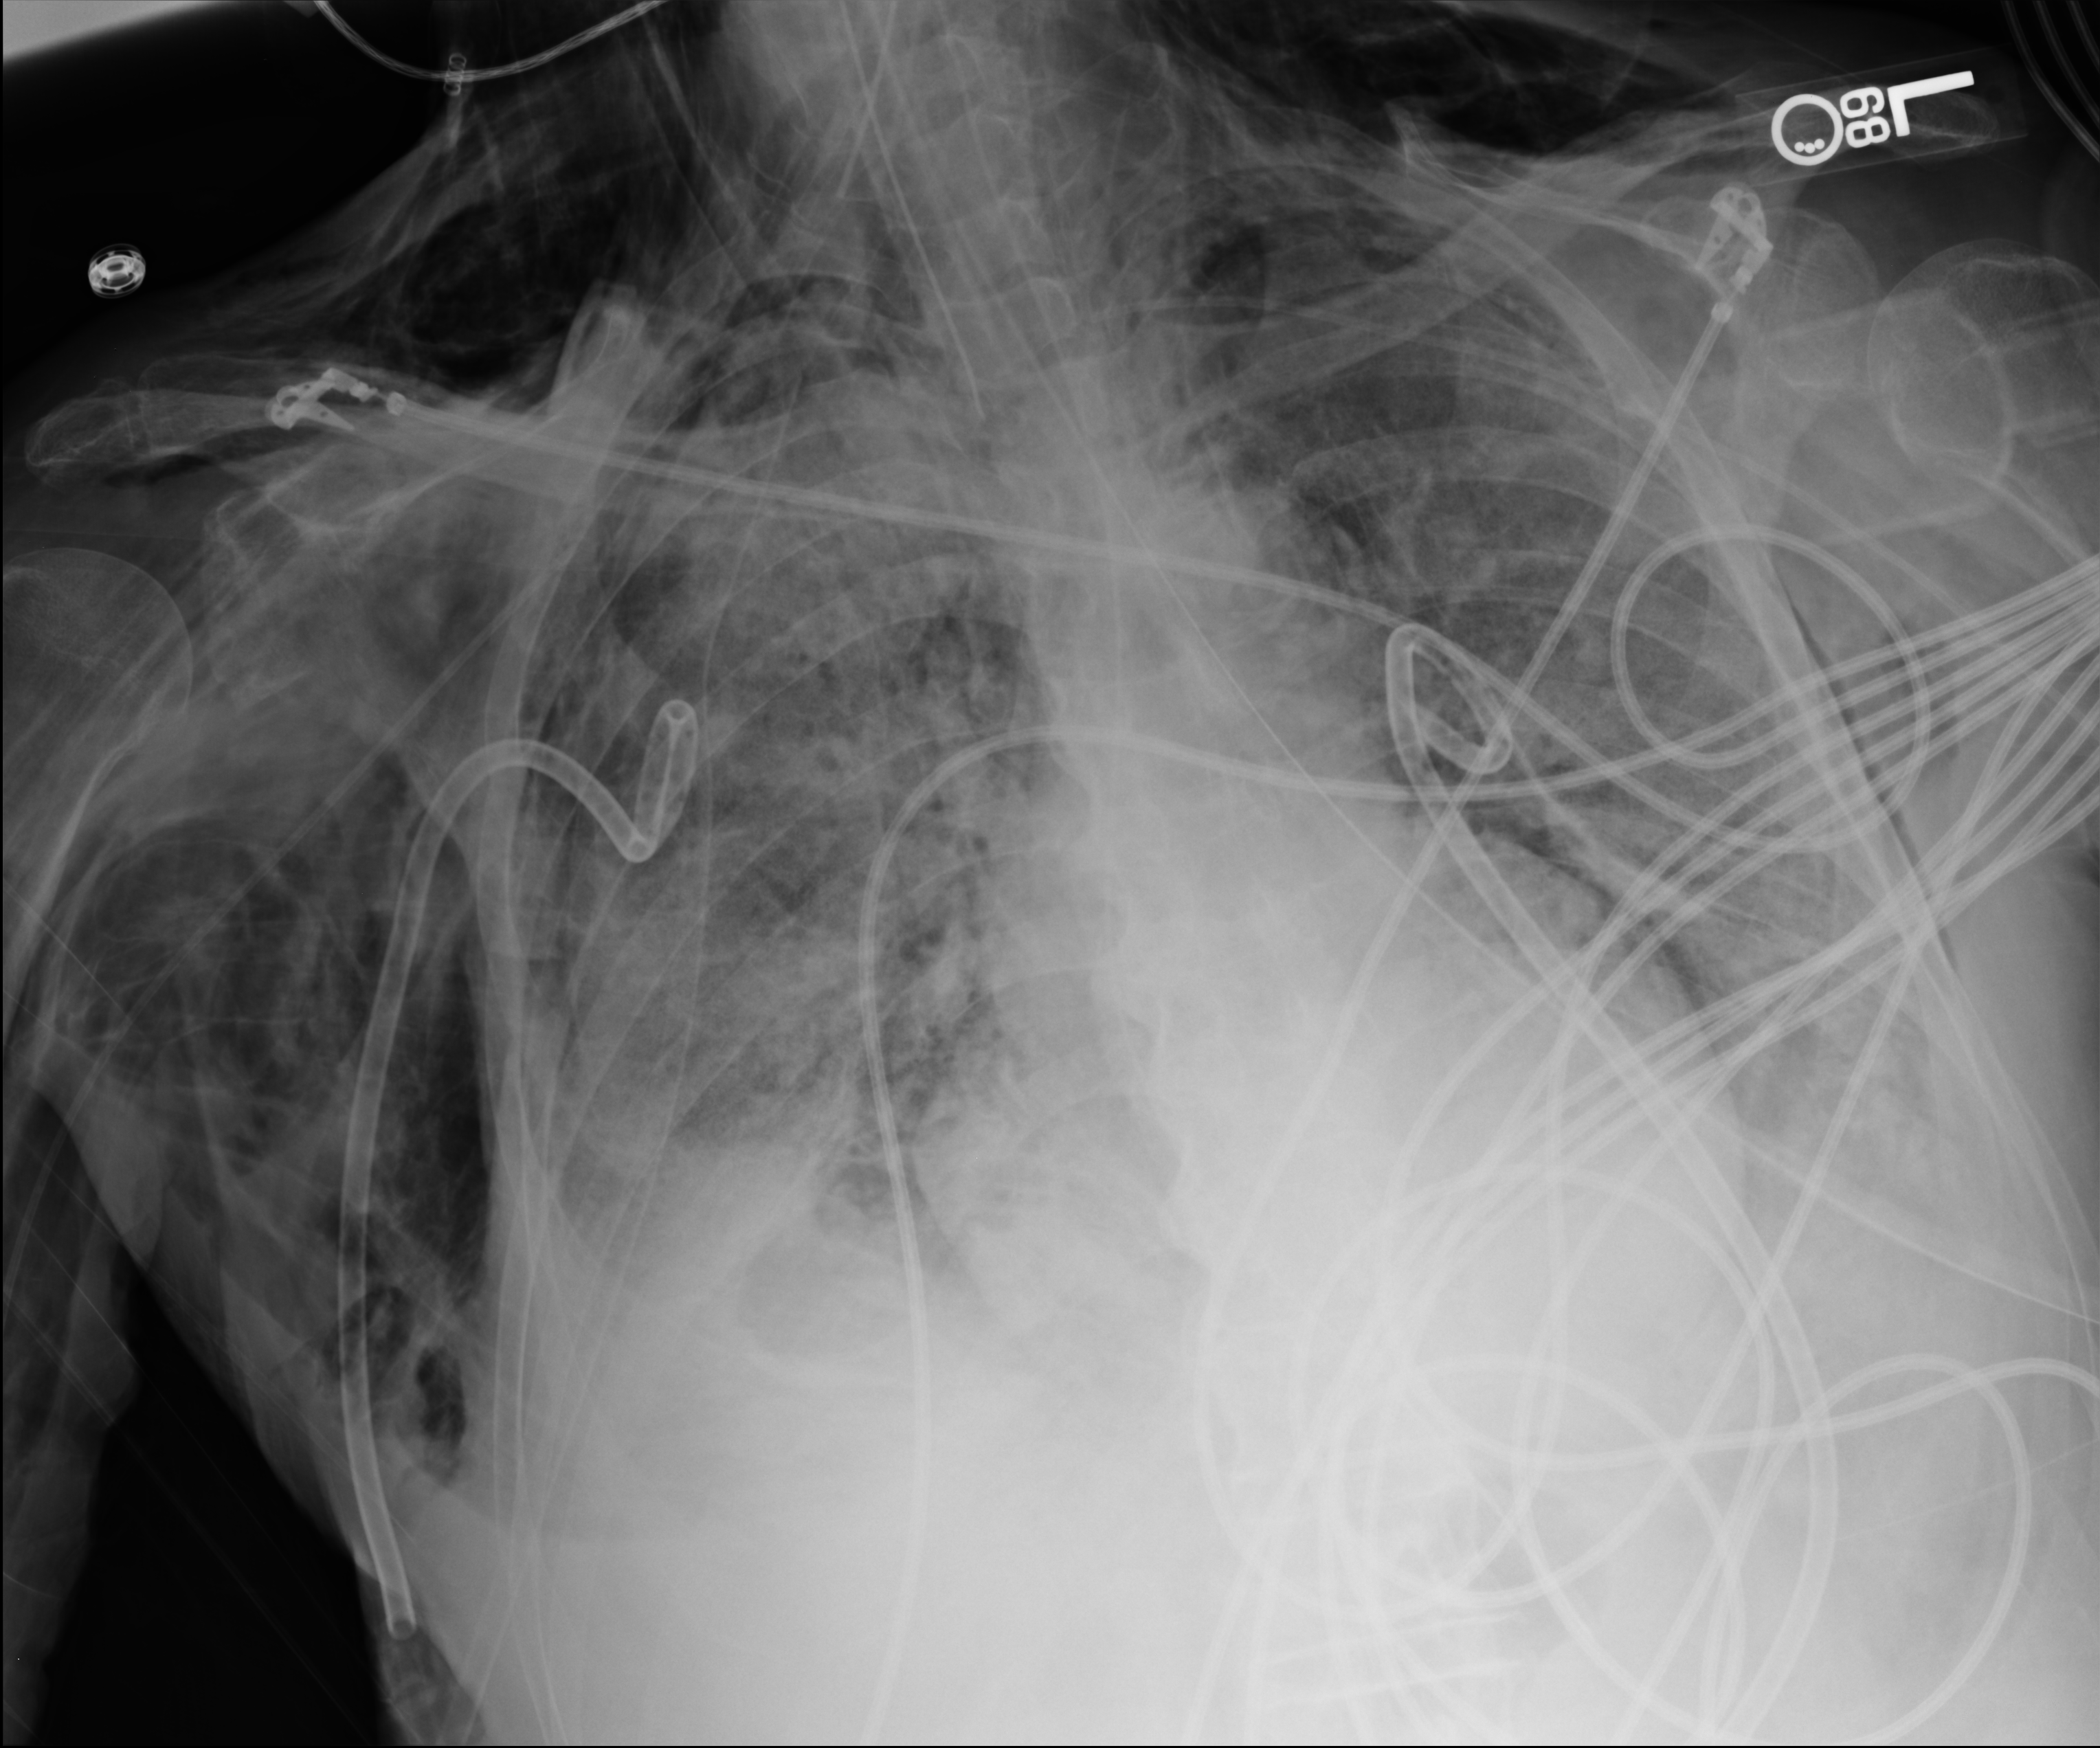
Portable chest radiograph; anteroposterior (AP) projection. Male patient hospitalised with COVID-19, age 75–90 years.
From the hospital-stay record, not from the radiograph (when in the stay this image was taken is not recorded): admitted to intensive care during this hospital stay: yes.